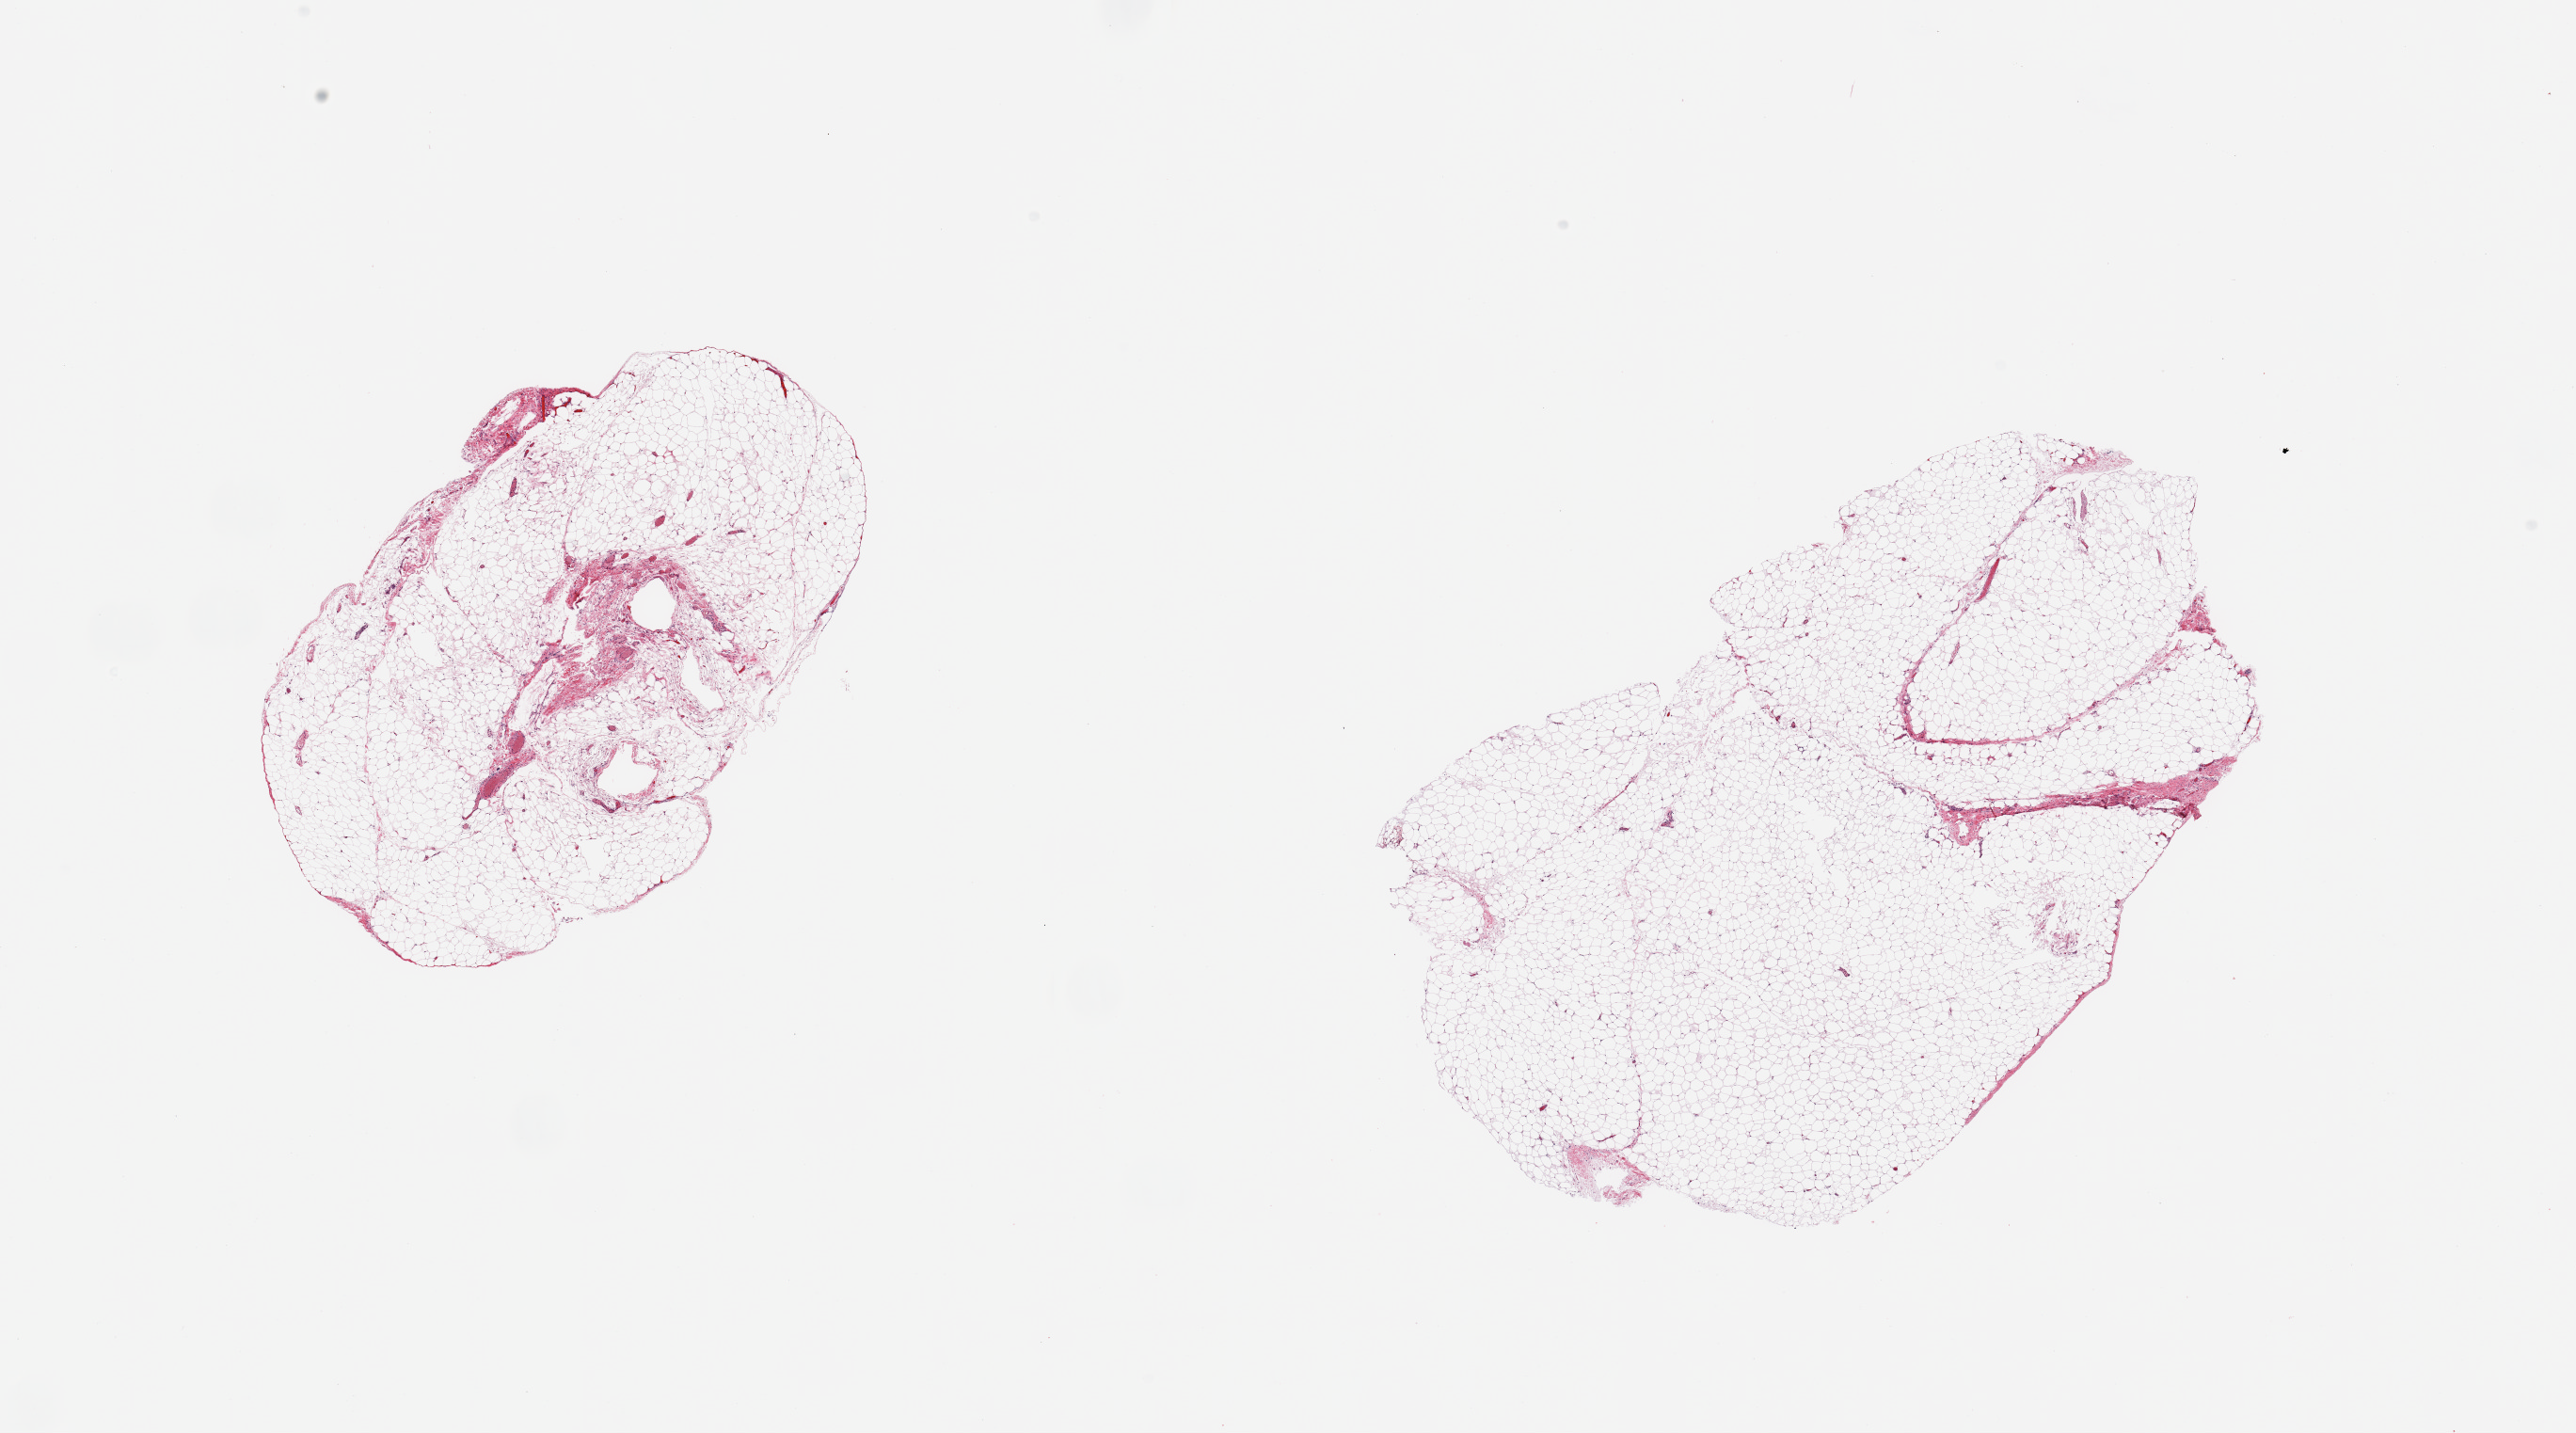
Whole-slide image, H&E stain, brightfield, low-resolution overview of the scanned area, about 21.7 x 12.0 mm; PAXgene-fixed paraffin-embedded (PFPE) section; section of omentum (target tissue); donor tissue sample. Donor: female.
Pathologist's review note for this sample: 2 pieces, fascia/vasular elements up to ~10% tissue.